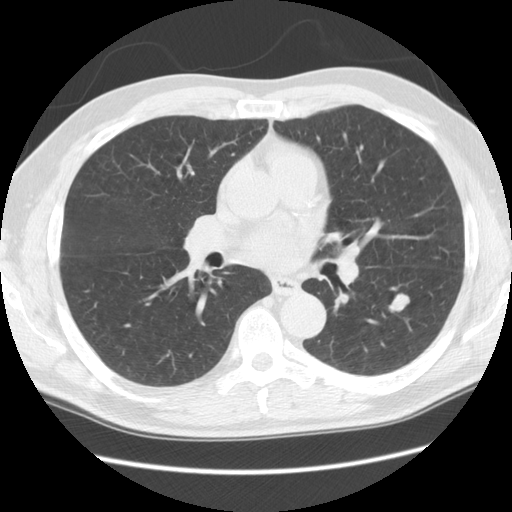
Chest CT (low-dose screening protocol), one axial image. Third screening round (two years after baseline). Lung window (W 1500 / L -600 HU). 2.5 mm slice thickness. Slice 56 of 111 in the series. 512 × 512 image matrix, field of view 370 × 370 mm. Male participant, aged 60 years at enrolment. Current smoker at enrolment.
• Expert reader's lesion annotation, bounding box (x1, y1, x2, y2) in pixels: (382, 289, 417, 319).
• The screening reader recorded 5 non-calcified nodules or masses ≥4 mm on this exam (left lower lobe, right lower lobe, right lower lobe, left lower lobe, left upper lobe); which of them this box marks is not recorded.
• Lung cancer was diagnosed 153 days after this screen: large cell neuroendocrine carcinoma, left lower lobe, poorly differentiated (G3), stage IB (AJCC 6th edition), 33 mm at pathology.